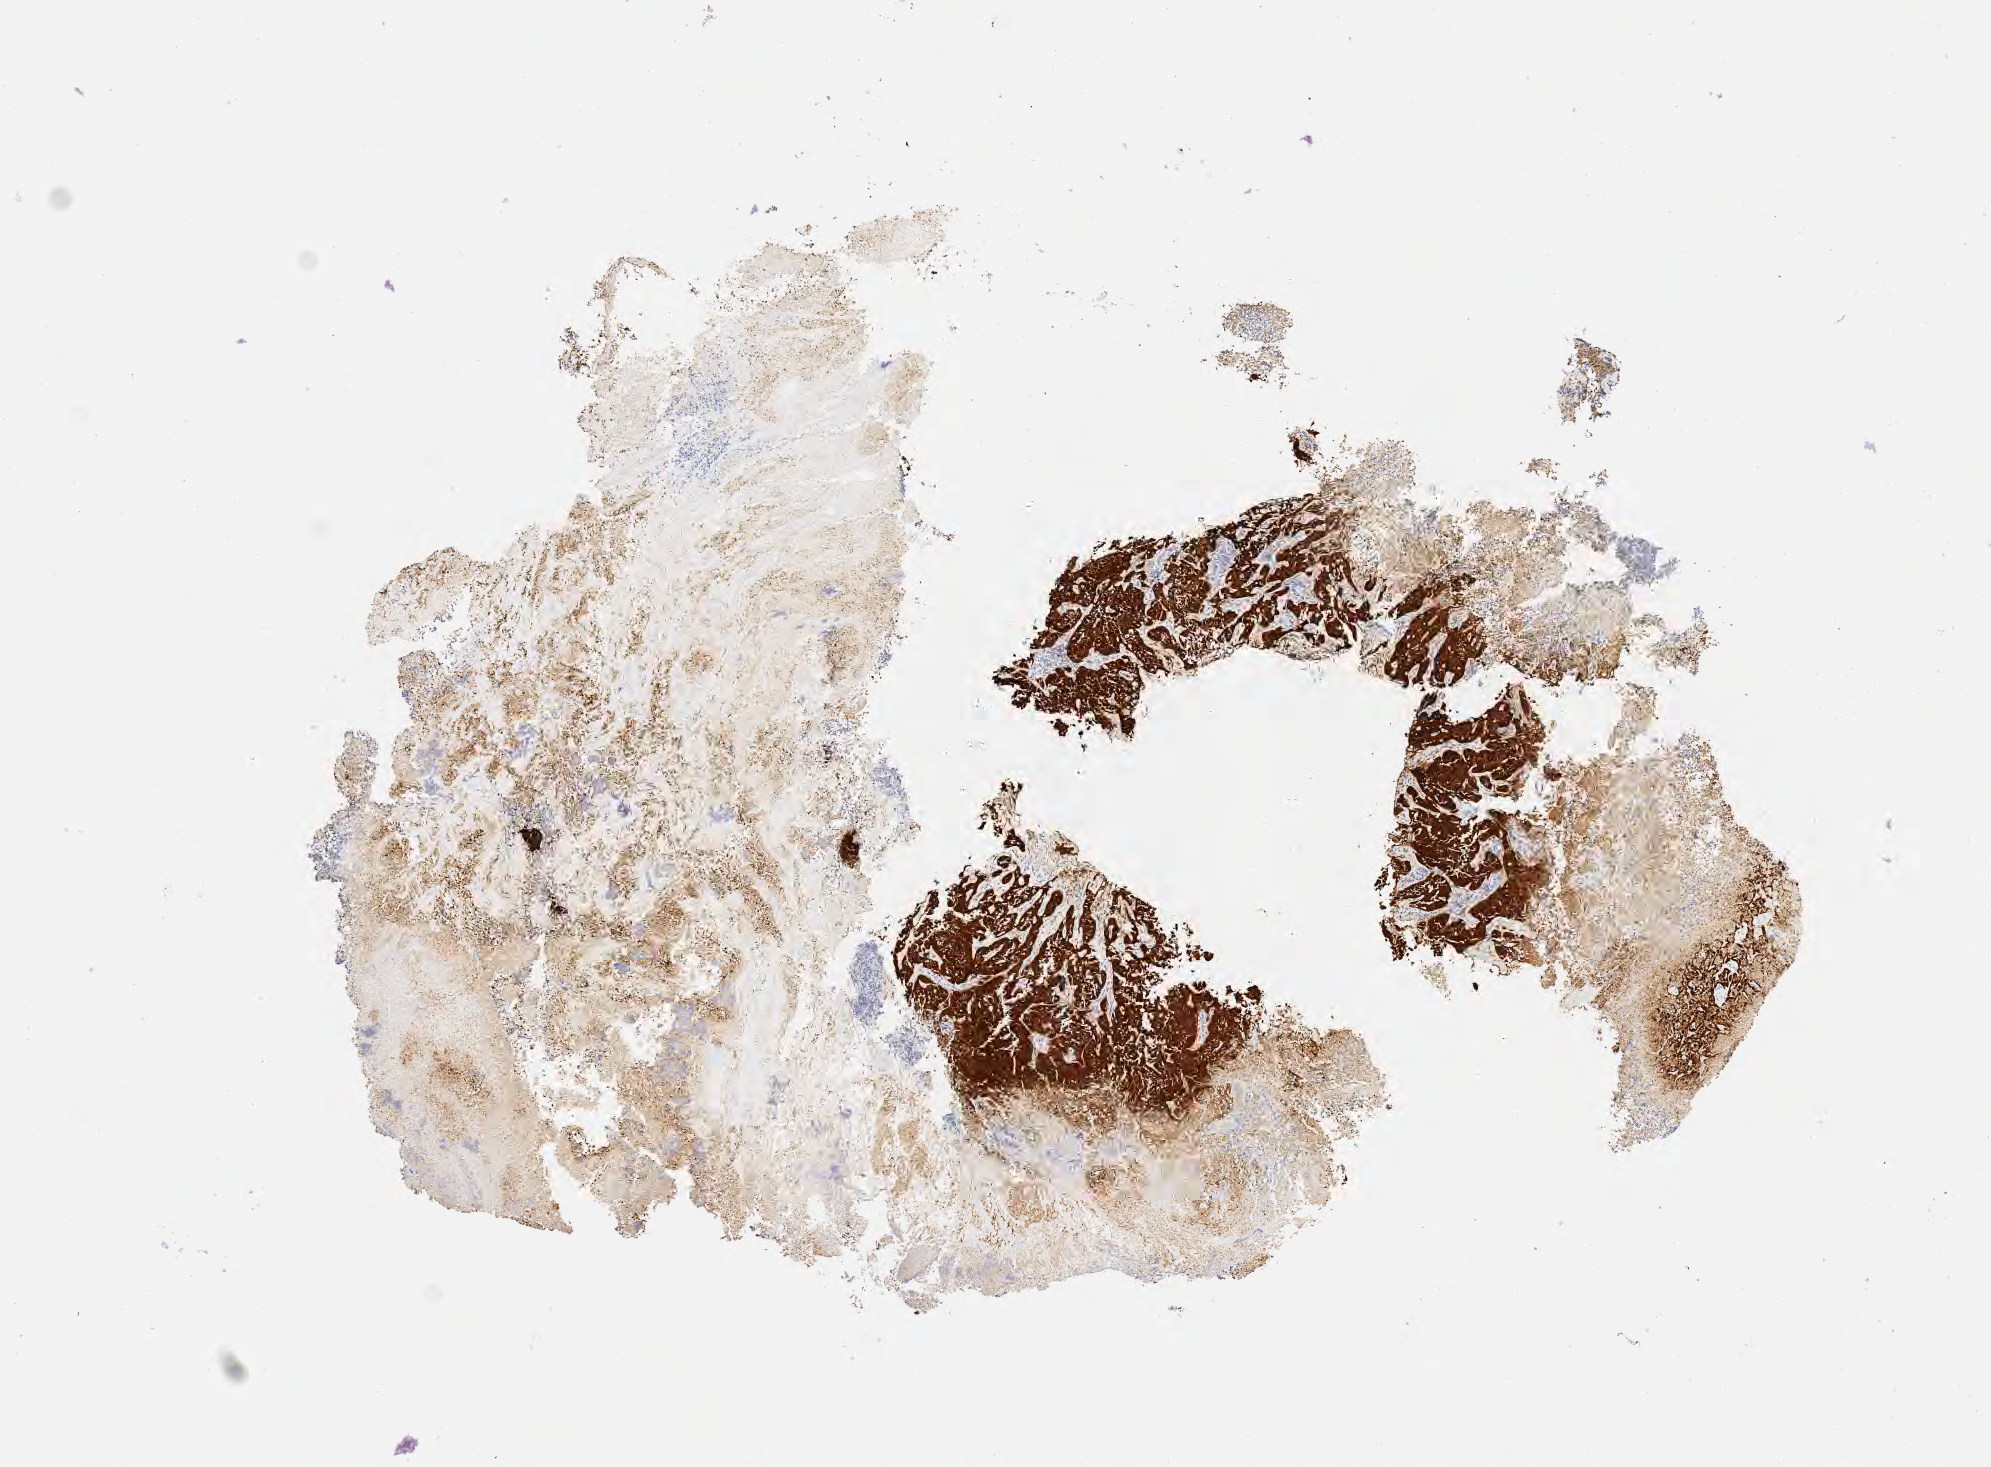
IHC for p16 (p16INK4a), whole-slide image — a low-resolution overview of the entire scanned area, about 8.1 x 5.9 mm, specimen: tumor tissue, site: cervix. Patient: female, 51 years old.
Diagnosis: Adenocarcinoma, NOS.